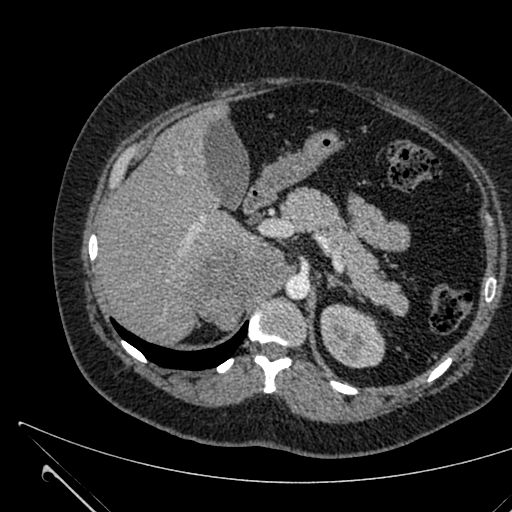
Contrast-enhanced abdominal CT, one axial slice. Position 440 of 731 along the scan axis. Soft-tissue window (W 400 / L 40 HU). 1 mm slice thickness. 512 × 512 image matrix, field of view 376 × 376 mm. Patient: female, 36 years. Case-level facts recorded for this patient, not image findings: diagnosis: adrenocortical carcinoma; tumour side: right adrenal; tumour size at pathology: 10 cm; Ki-67 index: 20 %; stage (as recorded): 4.
Structures marked on this image (semi-automatic segmentation, software-assisted and operator-edited):
- mass: bounding box [x1, y1, x2, y2] px = [191, 244, 285, 328]